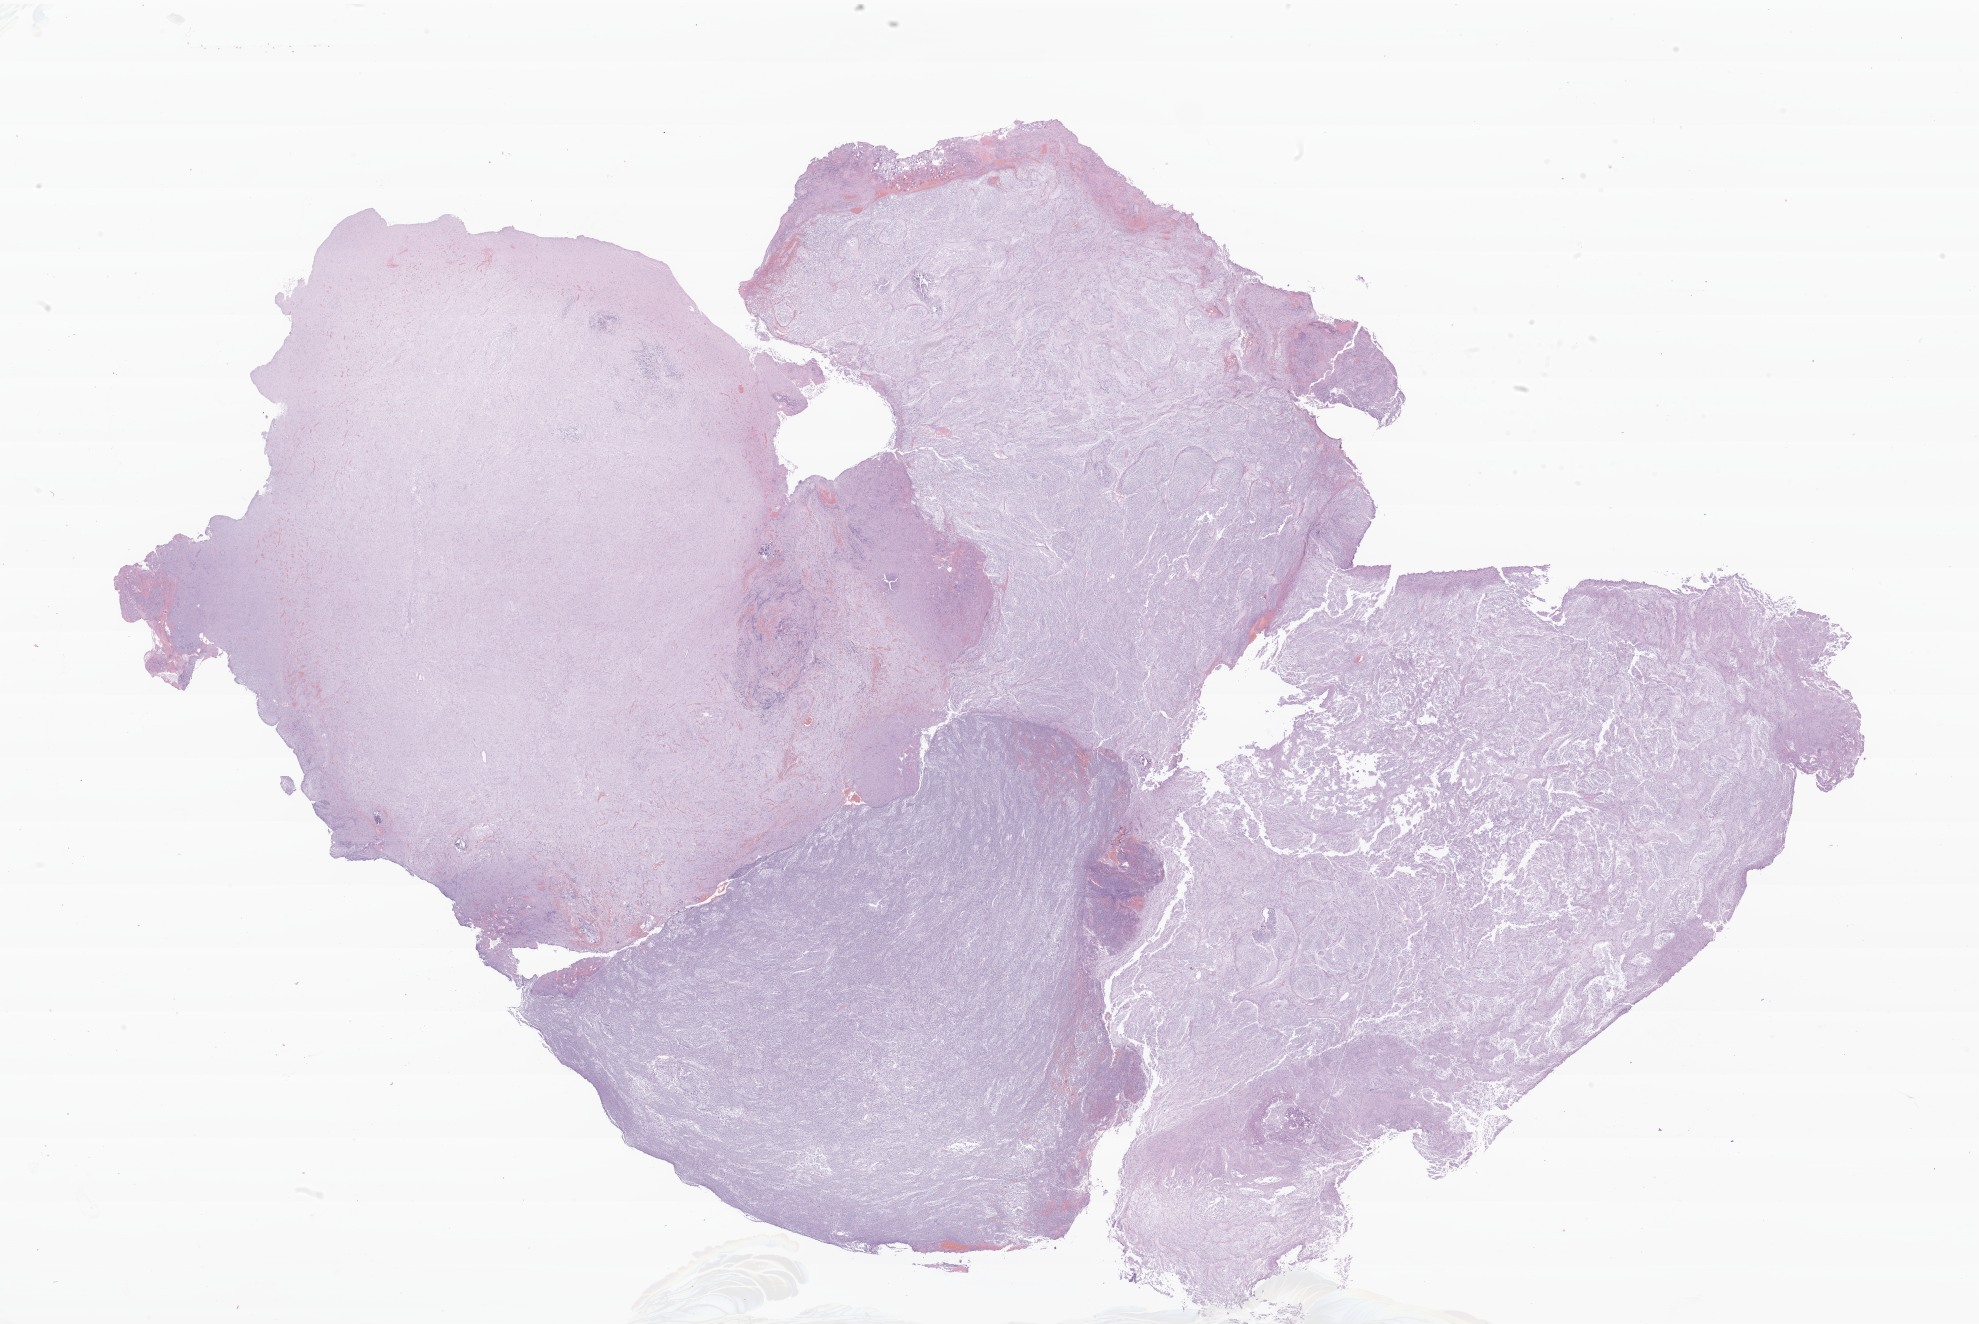
Digitized hematoxylin and eosin (H&E)-stained section of tumor tissue from the brain — low-resolution overview of the scanned area, about 33.3 x 22.3 mm. Formalin-fixed, paraffin-embedded (FFPE) tissue. Patient male; age 232 days.
Diagnosis: Medulloblastoma, NOS.